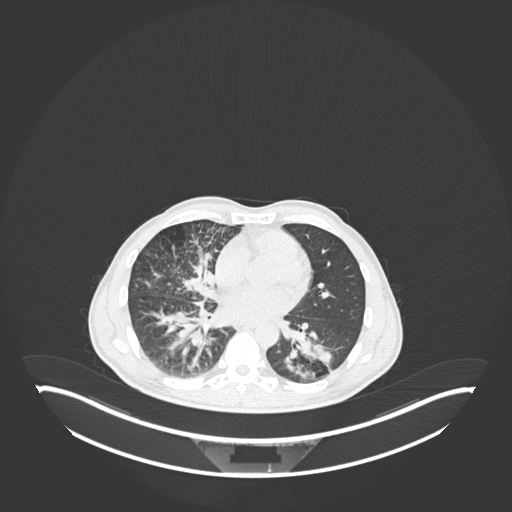
Chest CT, one axial slice; position 105 of 237 along the scan axis; 120 kVp; lung window (W 1500 / L -600 HU); 1 mm slice thickness; 512 × 512 image matrix, field of view 500 × 500 mm. Patient: male, 49 years. From the clinical record (not read from this slice): clinical TNM (as recorded): T2b N1 M0.
Structures marked on this image (rectangle marked by the reading radiologist):
- lung tumour (recorded histology: adenocarcinoma): box from (x=280, y=331) to (x=341, y=387) px